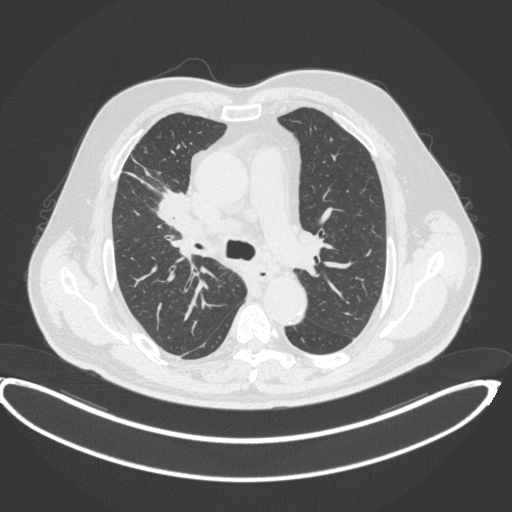
Chest CT, one axial slice; position 269 of 395 along the scan axis; 120 kVp; lung window (W 1500 / L -600 HU); 512 × 512 image matrix, field of view 448 × 448 mm. Patient: male, 62 years. From the clinical record (not read from this slice): clinical TNM (as recorded): T1c N3 M1c.
Structures marked on this image (bounding box drawn by a radiologist):
- lung tumour (recorded histology: adenocarcinoma): bounding box (x1, y1, x2, y2) in pixels: (152, 179, 195, 231)